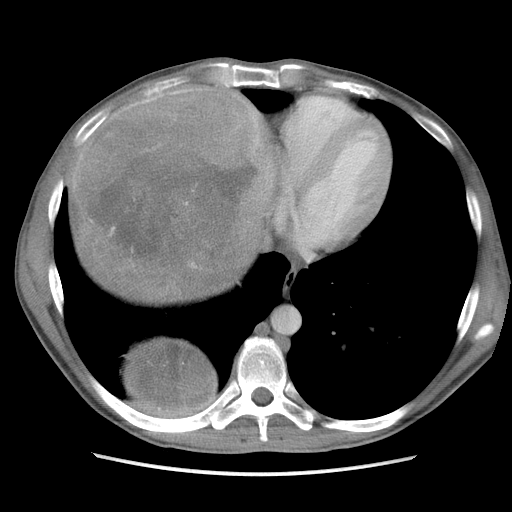
Contrast-enhanced abdominal CT, one axial slice; soft-tissue window (W 400 / L 40 HU); 5 mm slice thickness; 512 × 512 image matrix, field of view 360 × 360 mm. Male patient. From the clinical record (not read from this slice): diagnosis: adrenocortical carcinoma; tumour side: right adrenal; Ki-67 index: 13 %; stage (as recorded): 3.
Outlined on this slice (semi-automatically segmented with operator editing):
- mass: bounding box [x1, y1, x2, y2] px = [83, 86, 276, 418]